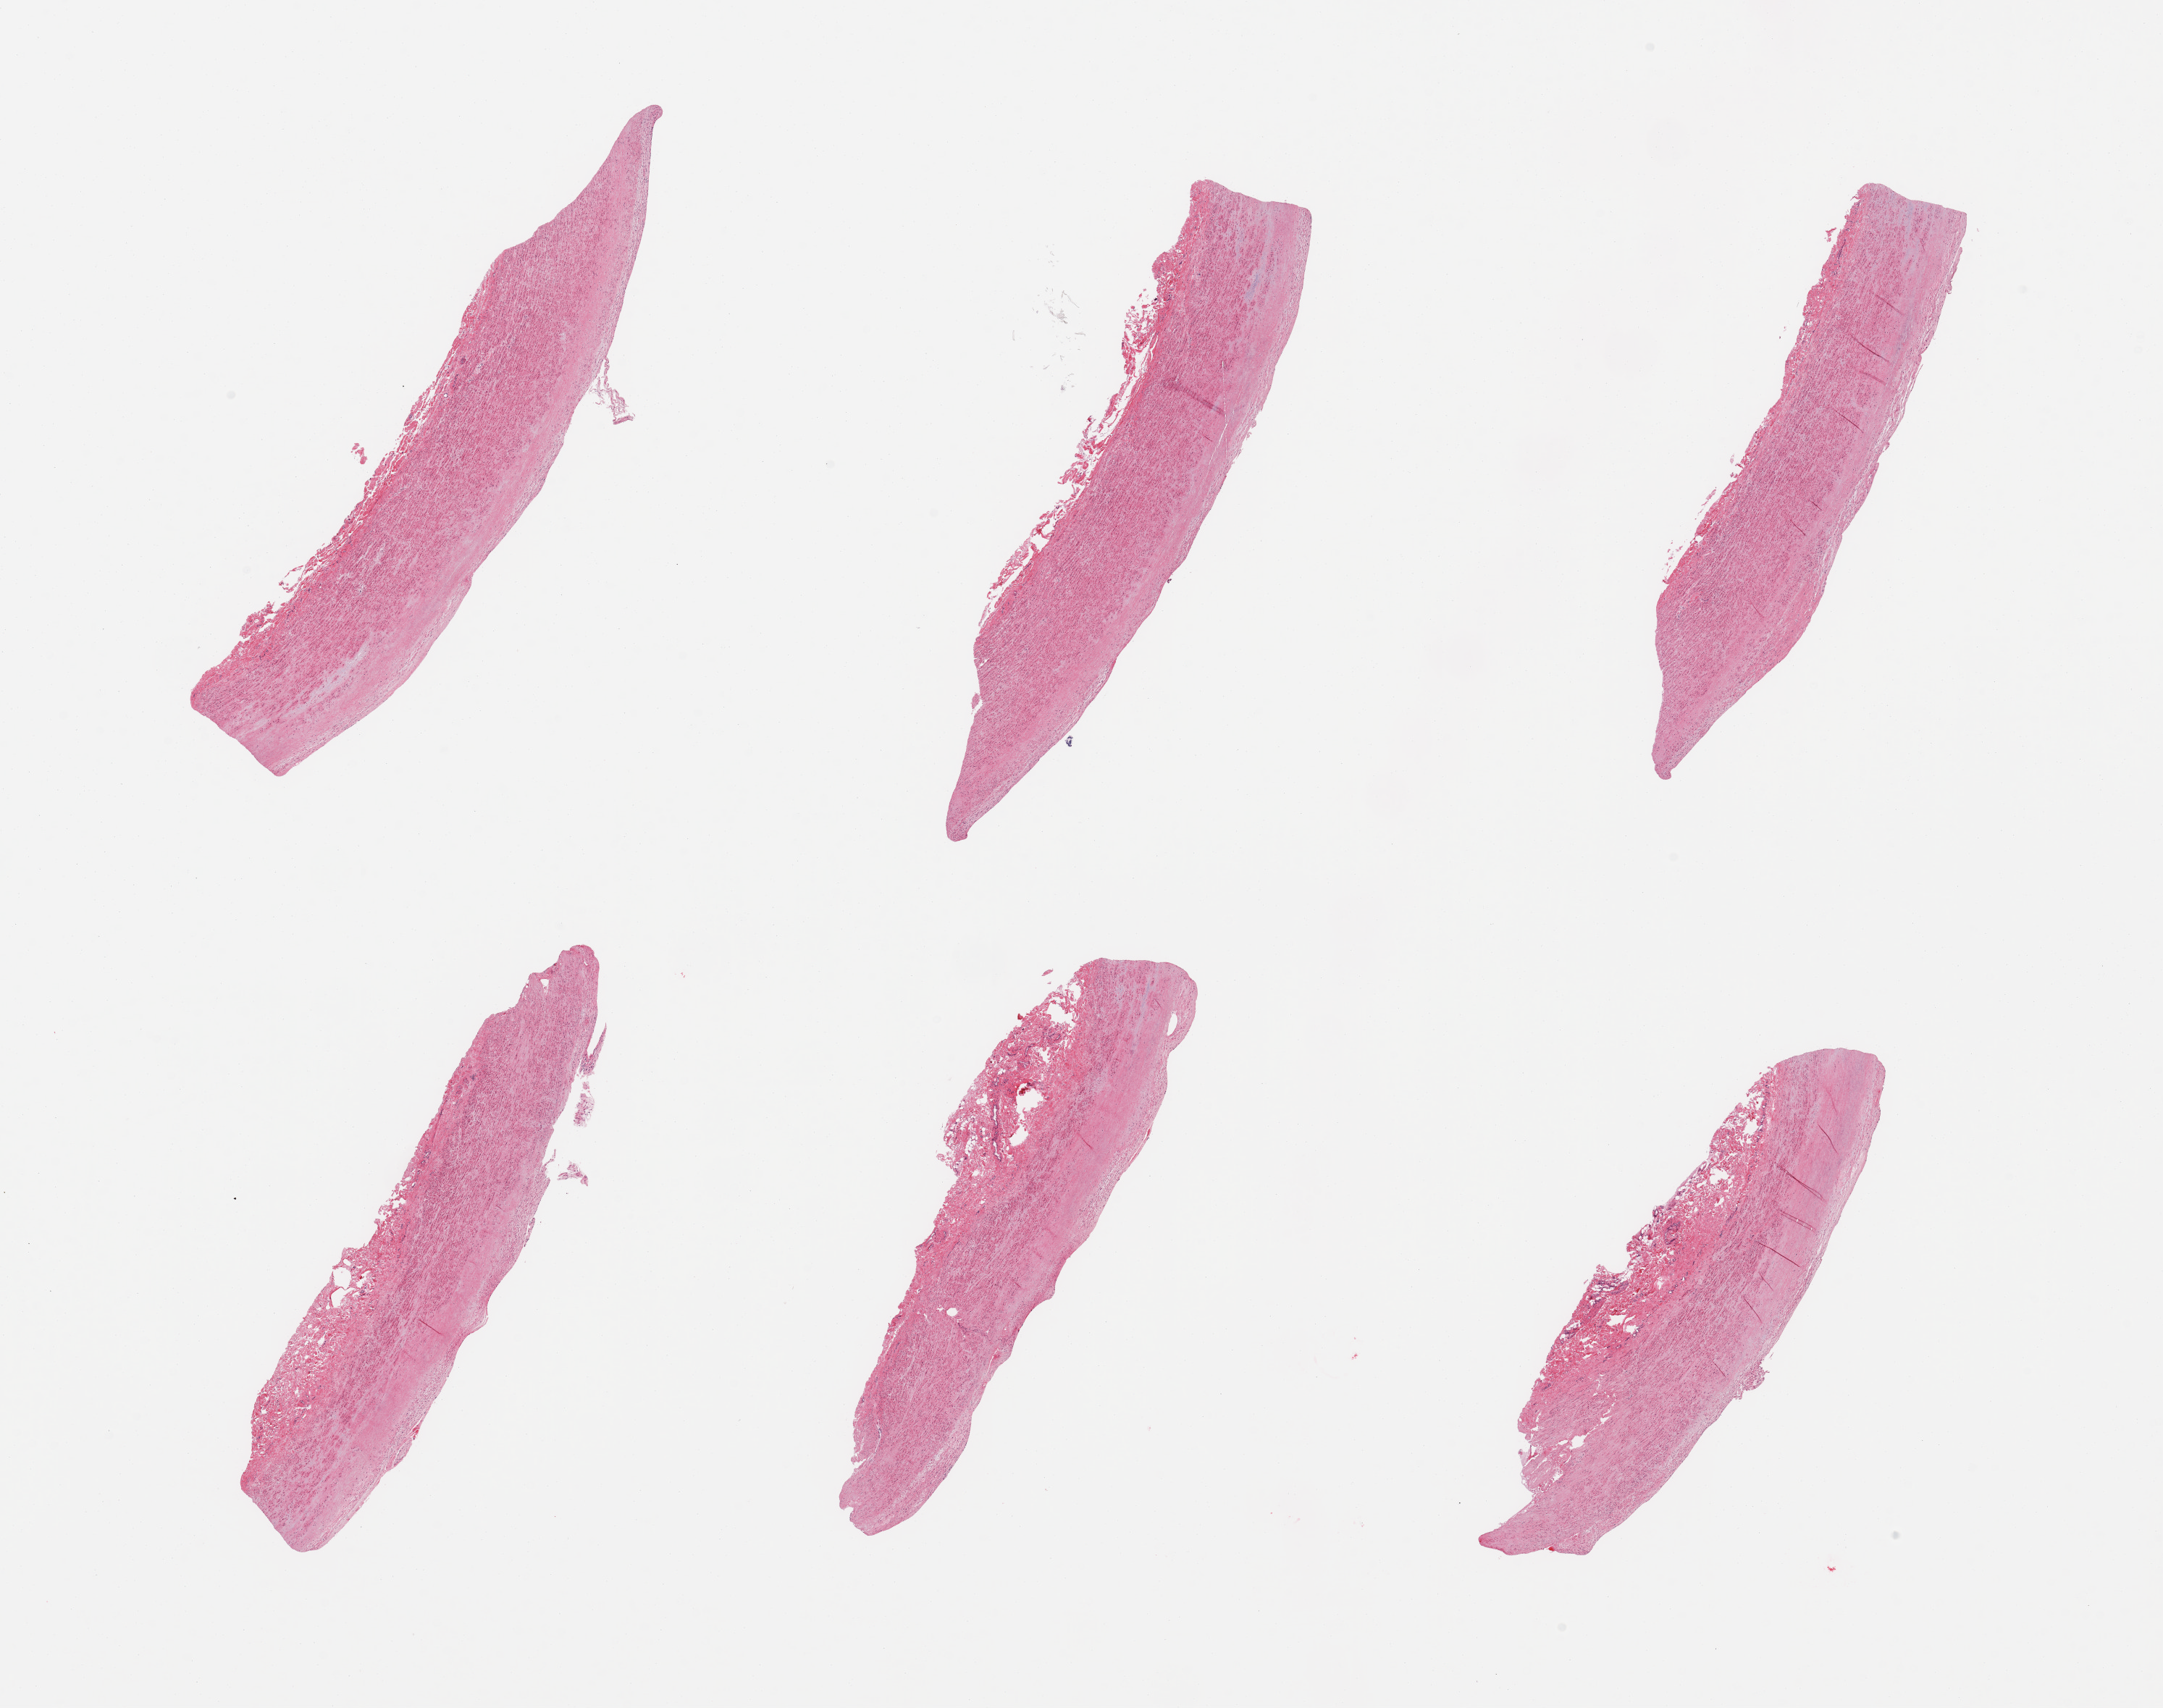
Whole-slide image, H&E stain — low-resolution overview of the scanned area, about 23.6 x 18.7 mm. PAXgene-fixed paraffin-embedded (PFPE) section. Target tissue: aorta. Donor tissue sample. Donor sex: male.
Reviewer comment on this tissue sample: 6 pieces, minimal atherosis.